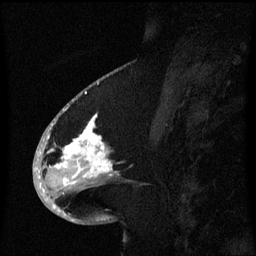
Breast MRI (dynamic contrast-enhanced), one sagittal slice; position 29 of 60 along the scan axis; dynamic contrast-enhanced series, image 2 of 3 at this slice position (ordered by acquisition); 1.5 T; TE 4.2 ms, TR 8.4 ms; 2.1 mm slice thickness; 256 × 256 image matrix. Female patient, age 53 years. From the clinical record (not read from this slice): setting: breast cancer imaged before/during neoadjuvant chemotherapy; receptor status: HR-positive, HER2-negative.
Outlined on this slice (semi-automatically segmented with operator editing):
- analysis volume of interest (the breast-tissue region the enhancement analysis was run in; not a lesion): bounding box <49,108,120,201> (left, top, right, bottom; pixels)
- tumour enhancement mask (voxels above the 70 % enhancement threshold inside the analysis volume of interest): <49,116,113,177>